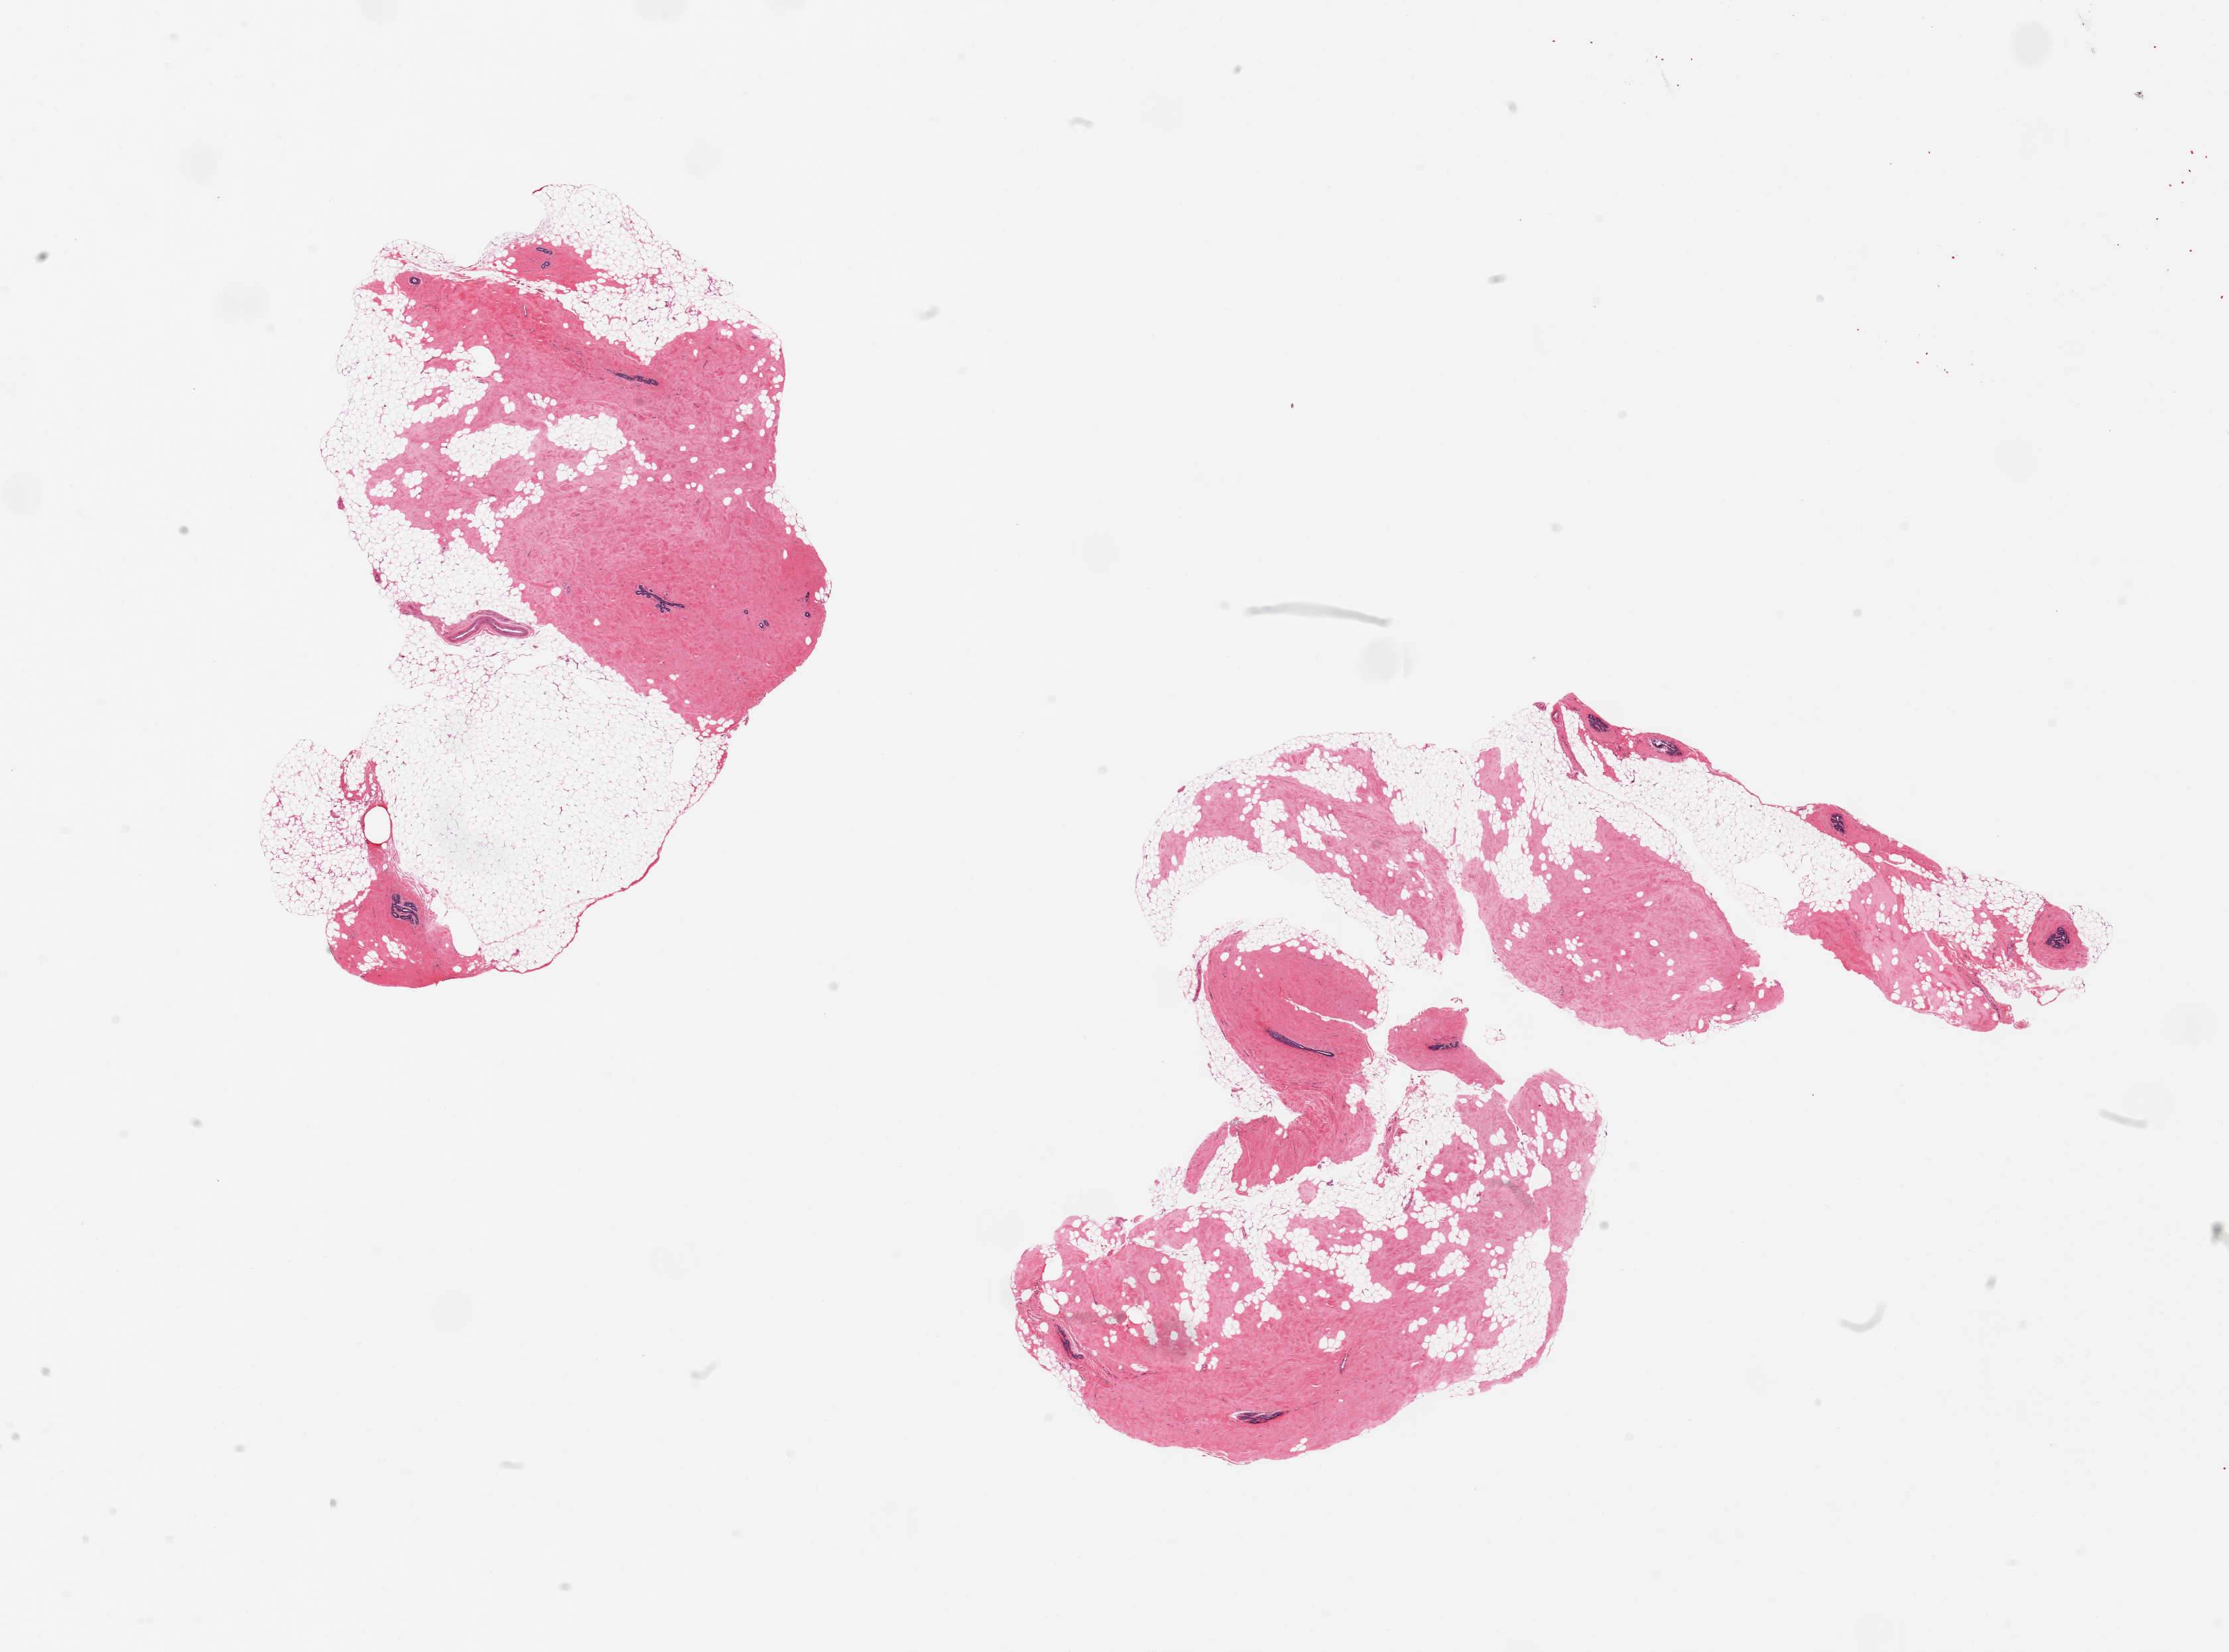
Whole-slide image, haematoxylin and eosin stain, a low-resolution overview of the entire scanned area, about 26.6 x 19.7 mm, PAXgene-fixed paraffin-embedded (PFPE) section, section of breast (target tissue), donor tissue sample.
Reviewer comment on this tissue sample: 2 pieces, atrophic ductal/lbular elements, fibrocystic changes.